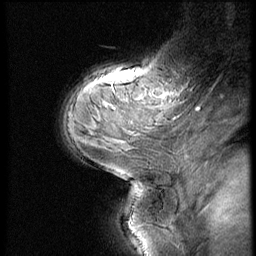
Breast MRI (dynamic contrast-enhanced), one sagittal slice. Position 40 of 56 along the scan axis. 3 images stored at this slice position (order not interpretable as contrast timing). 1.5 T. TE 4.2 ms, TR 9 ms. 2.5 mm slice thickness. 256 × 256 image matrix. Female patient, age 54 years. From the clinical record (not read from this slice): setting: breast cancer imaged before/during neoadjuvant chemotherapy; receptor status: triple-negative.
Structures marked on this image (semi-automatic segmentation, software-assisted and operator-edited):
- analysis volume of interest (the breast-tissue region the enhancement analysis was run in; not a lesion): bounding box <141,76,199,121> (left, top, right, bottom; pixels)
- tumour enhancement mask (voxels above the 140 % enhancement threshold inside the analysis volume of interest): <170,92,176,94>